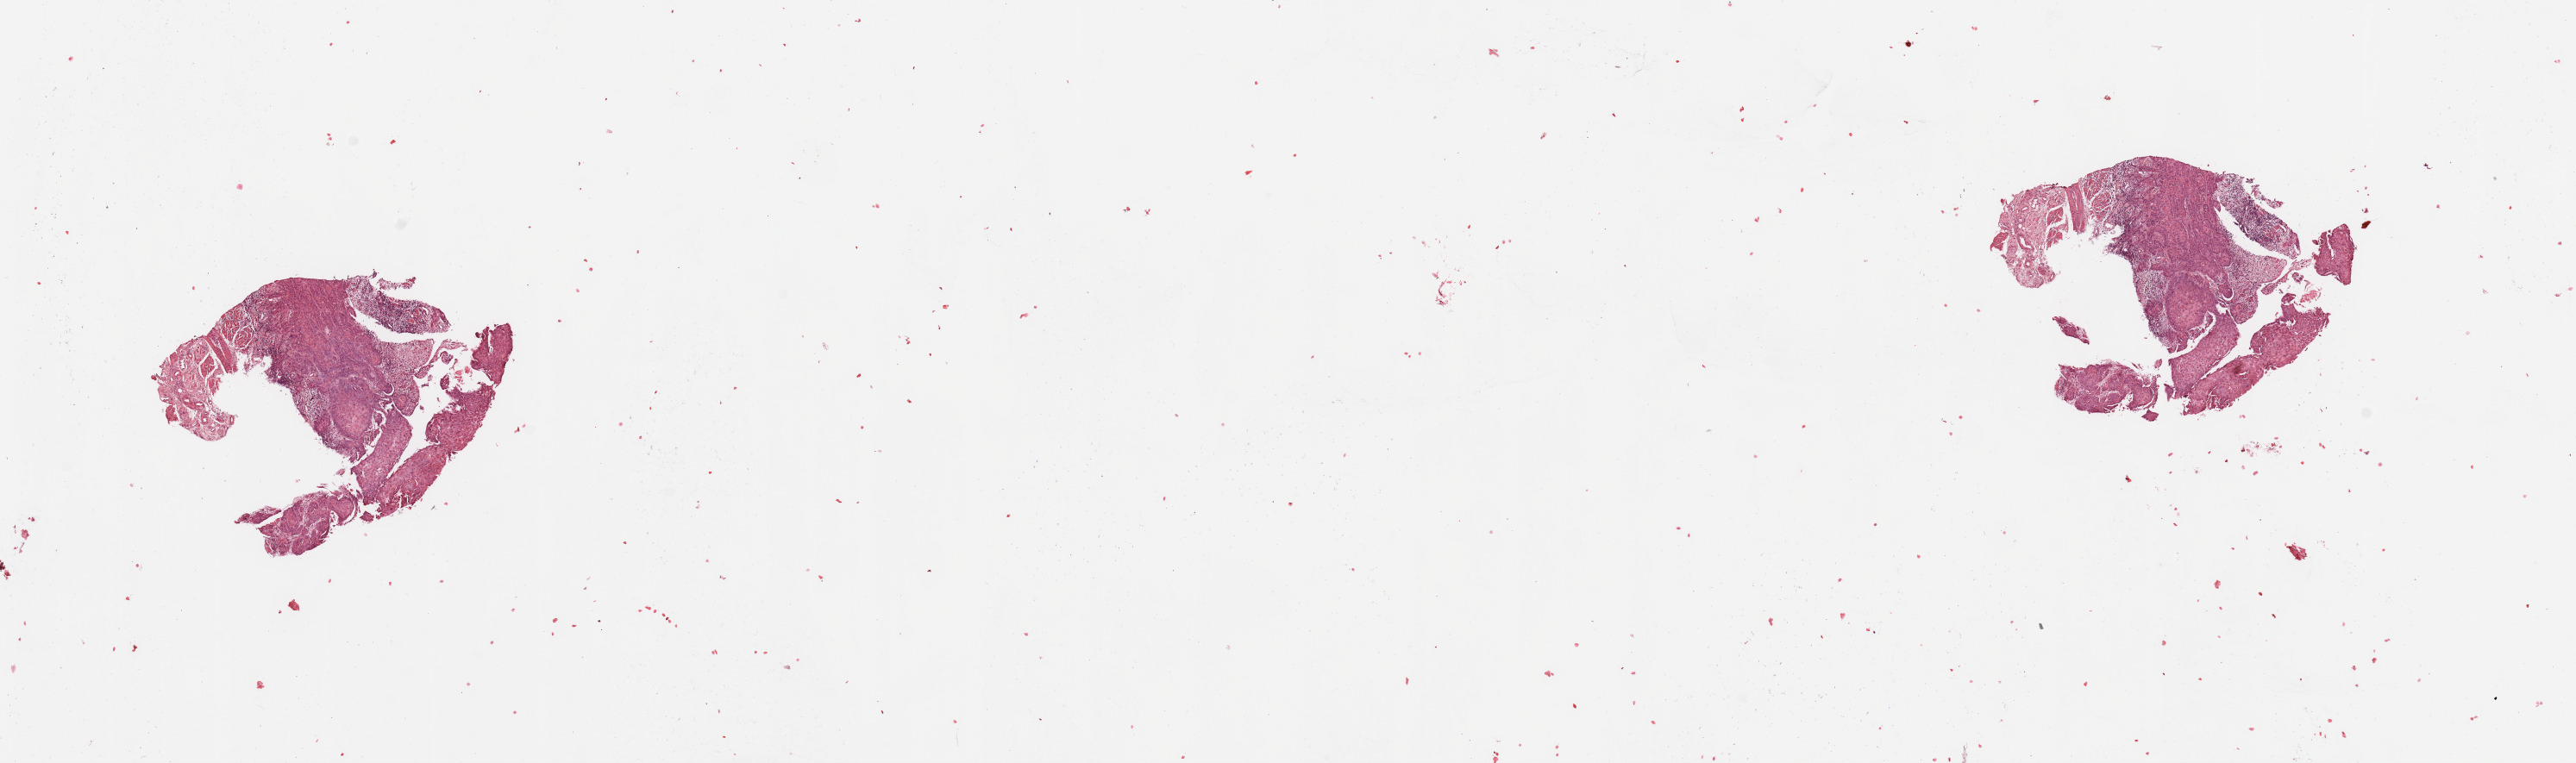
Digitized H&E-stained tissue section (whole slide), a low-resolution overview of the entire scanned area, about 23.6 x 7.0 mm (from a 20x scan). Tumour tissue sample, sampled site: tongue. Male, 53 y/o. Histologic grade: G2 (moderately differentiated). Pathologist review of this section (percent, as recorded): tumour nuclei 80%, necrosis 5%.
AJCC pathologic stage: II. Histologic diagnosis: Squamous cell carcinoma, NOS (tongue, NOS).